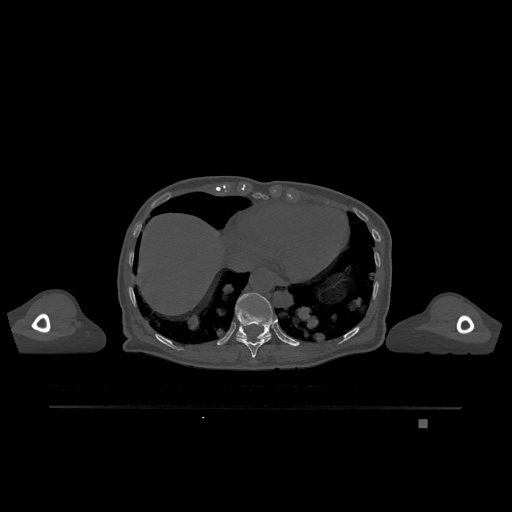
CT including the spine, one axial slice. Bone window (W 1800 / L 400 HU). 512 × 512 image matrix. Female patient, age 74 years. Case-level facts recorded for this patient, not image findings: primary cancer: lung; vertebrae with lytic lesions (as recorded): T1, T4, T5, T6, L4, L5.
Annotated regions visible in this slice (semi-automatic segmentation, software-assisted and operator-edited):
- T10 vertebra: bounding box [x1, y1, x2, y2] px = [236, 337, 271, 358]
- T11 vertebra: [235, 292, 277, 339]